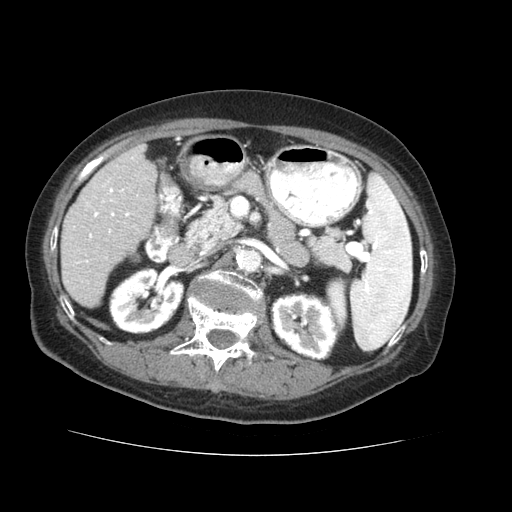
Contrast-enhanced abdominal CT (liver protocol), one axial slice; position 19 of 73 along the scan axis; reconstruction kernel STANDARD; 120 kVp; soft-tissue window (W 400 / L 40 HU); 2.5 mm slice thickness; 512 × 512 image matrix, field of view 360 × 360 mm. Case-level facts recorded for this patient, not image findings: diagnosis: hepatocellular carcinoma (patient treated with transarterial chemoembolisation; whether this scan precedes or follows treatment is not stated here); TNM stage (as recorded): Stage-IVB; Child-Pugh class: A.
Annotated regions visible in this slice (semi-automatically segmented with operator editing):
- liver parenchyma outside the tumour (the mass and vessels are separate outlines, so this box may not span the whole liver): bounding box (x1, y1, x2, y2) in pixels: (60, 144, 156, 306)
- liver vessels: (74, 157, 134, 264)